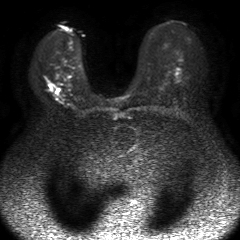
Breast MRI, one axial slice; slice 30 of 50 in the series (ordered by position); diffusion-weighted series; image 2 of 4 stored at this slice position (different b-values; order by instance number); 1.5 T; 4 mm slice thickness; 240 × 240 image matrix, field of view 330 × 330 mm. Female patient.
Annotated regions visible in this slice (manually delineated by an expert):
- tumour on diffusion-weighted imaging: bounding box <50,88,57,94> (left, top, right, bottom; pixels)